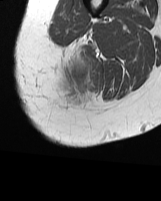
MRI of an extremity soft-tissue mass, one axial slice; slice 12 of 70 in the series (ordered by position); MR volume resampled by the dataset authors to the PET/CT grid (not the native acquisition matrix); 3.27 mm slice thickness; 161 × 201 image matrix. Female patient. From the clinical record (not read from this slice): histological type: synovial sarcoma; grade: intermediate; site of the primary tumour: right buttock.
Structures marked on this image (expert contour drawn on MRI and transferred to this co-registered scan by the dataset authors):
- gross tumour volume including surrounding oedema: bounding box (x1, y1, x2, y2) in pixels: (63, 47, 93, 101)
- gross tumour volume (mass): (69, 65, 87, 80)